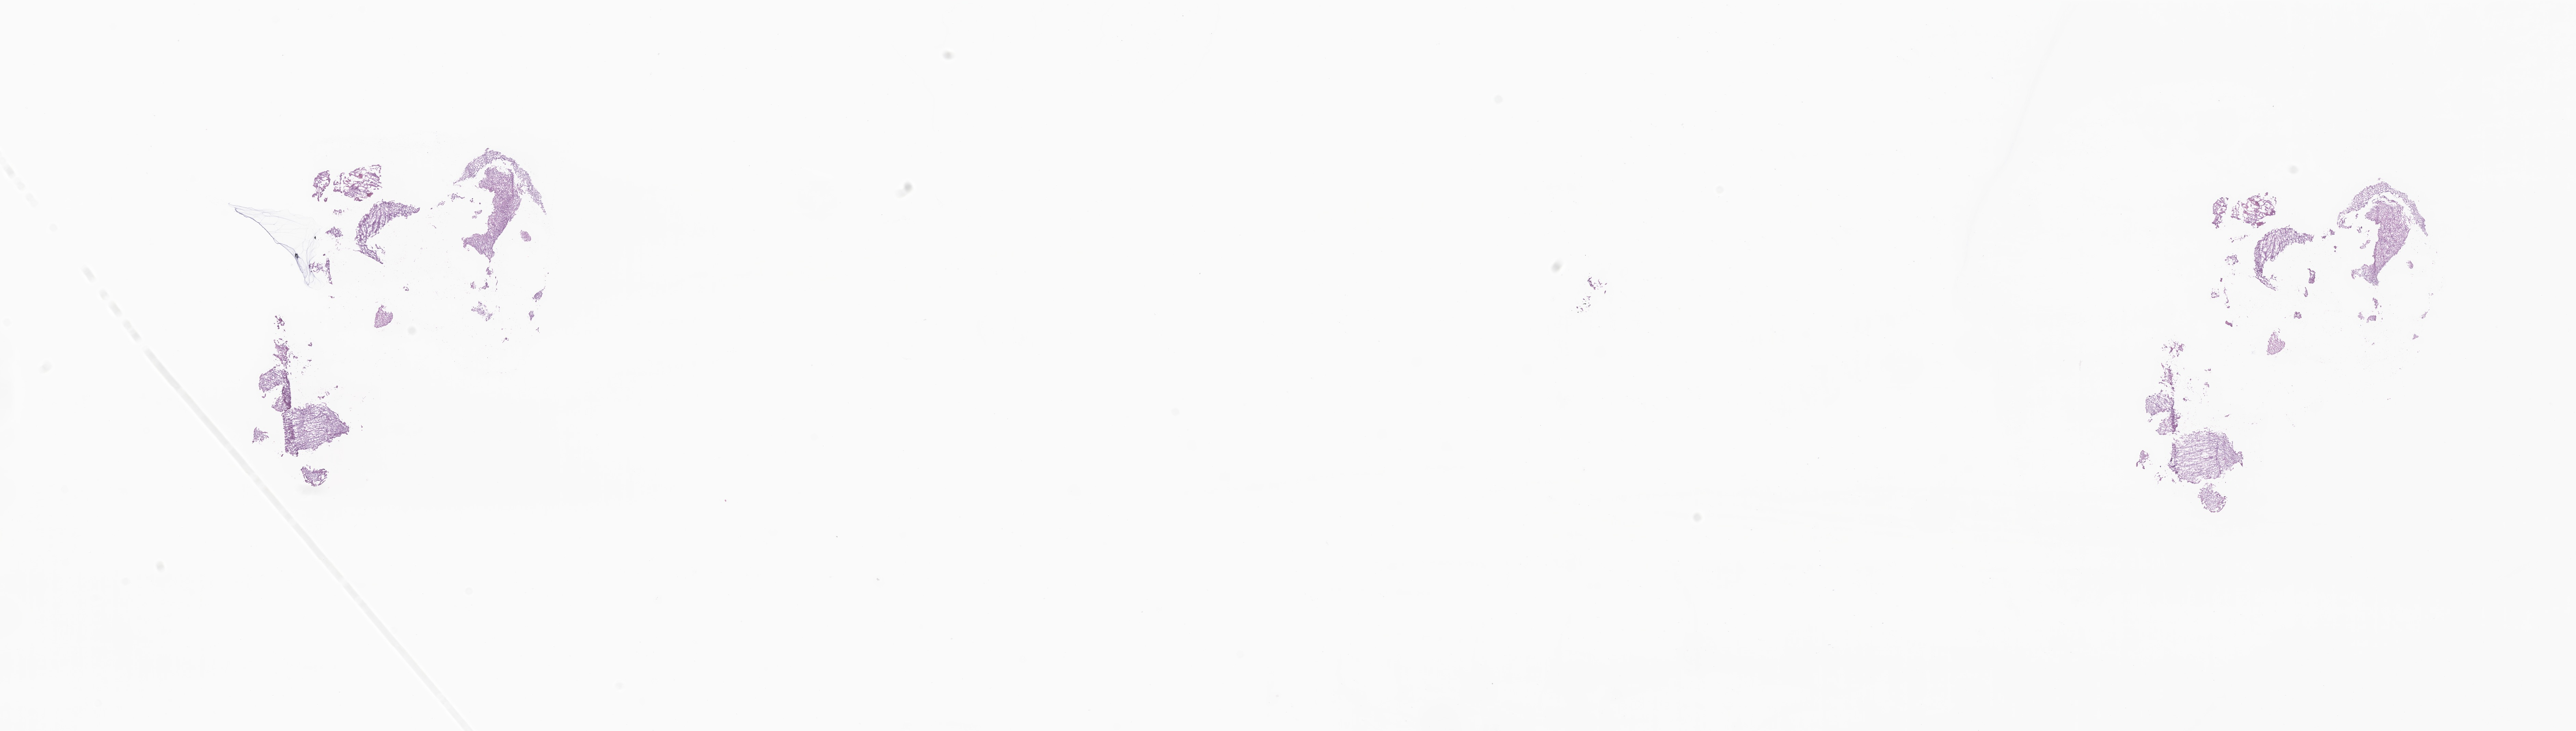
Digitized H&E-stained section of tumor tissue from the cerebellum, low-resolution overview of the scanned area, about 31.8 x 9.0 mm; cryosection (OCT / tissue freezing medium). Patient: male, age 86 months (7 years 2 months).
Diagnosis: Astrocytoma, NOS.